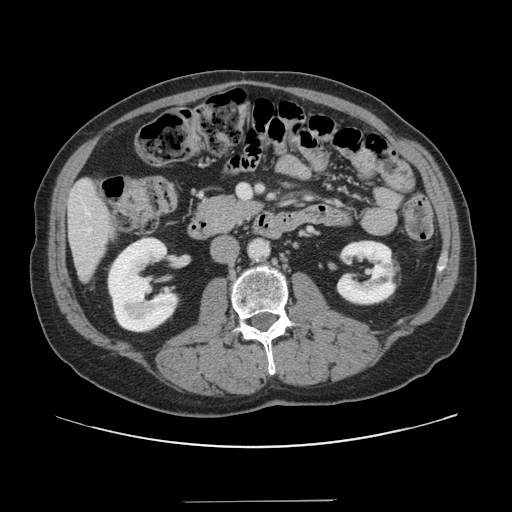
Contrast-enhanced abdominal CT, one axial slice; slice 47 of 151 in the series (ordered by position); 120 kVp; intravenous contrast given; soft-tissue window (W 400 / L 40 HU); 512 × 512 image matrix, field of view 399 × 399 mm. Male patient, age 63 years. From the clinical record (not read from this slice): diagnosis: colorectal cancer liver metastases, imaged before liver resection; multiple liver metastases: no; largest metastasis: 2.1 cm; disease in both lobes: no.
Annotated regions visible in this slice (expert manual segmentation):
- liver: box from (x=69, y=181) to (x=113, y=278) px
- planned liver remnant (the part of the liver to remain after resection): (x=69, y=181)–(x=115, y=279)
- portal vein (with intrahepatic branches): (x=239, y=185)–(x=250, y=198)